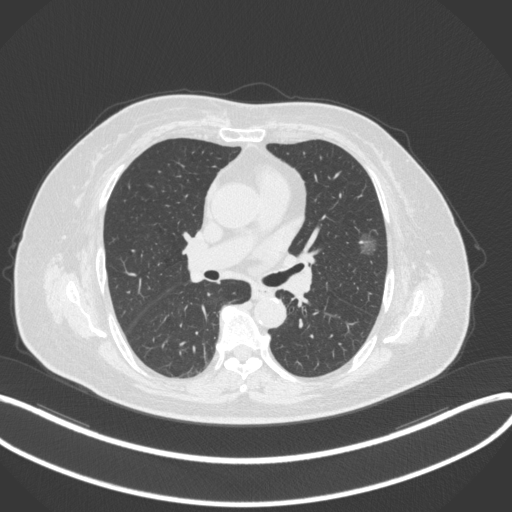
Chest CT, one axial slice. Slice 175 of 286 in the series (ordered by position). Reconstruction kernel B31f. 120 kVp. Lung window (W 1500 / L -600 HU). 1 mm slice thickness. 512 × 512 image matrix. Patient: female, 76 years. Case-level facts recorded for this patient, not image findings: clinical TNM (as recorded): T1b N0 M0; histopathological grade: G1-2.
Outlined on this slice (rectangle marked by the reading radiologist):
- lung tumour (recorded histology: adenocarcinoma): bounding box <355,225,381,260> (left, top, right, bottom; pixels)